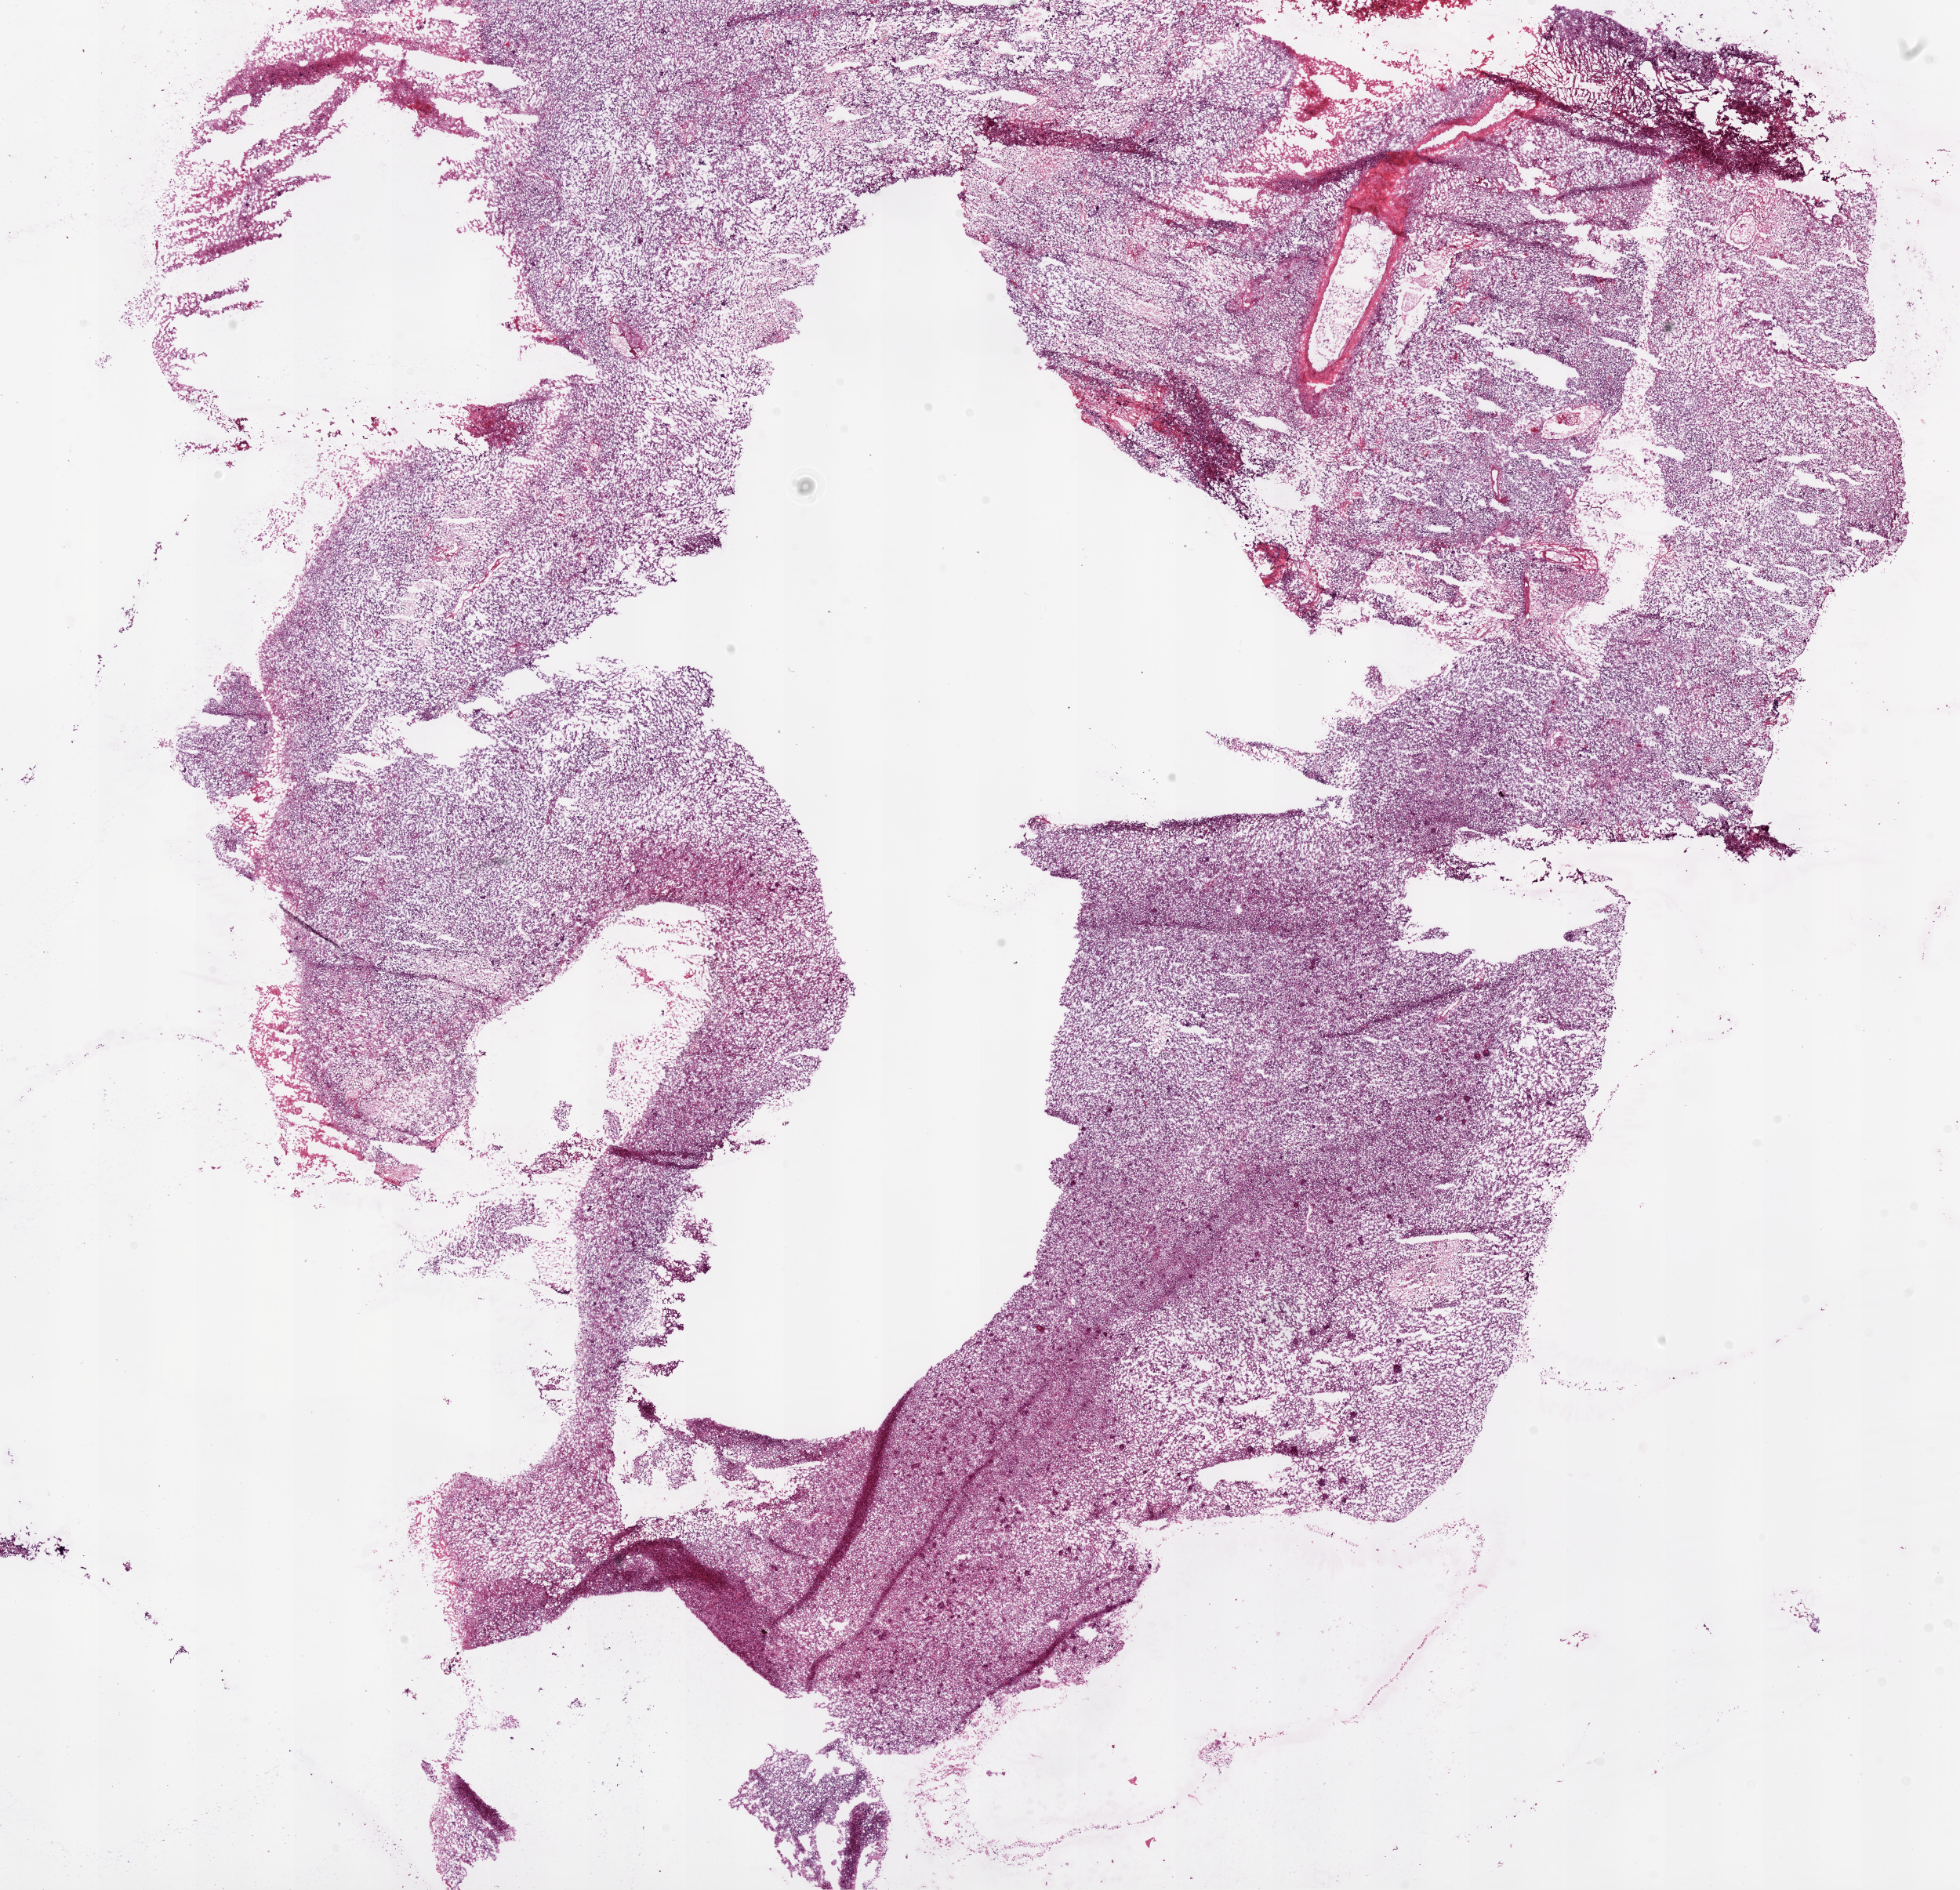
Whole-slide histology image, Hematoxylin and eosin (H&E) stained, whole scanned area (about 20.1 x 19.3 mm, from a 20x scan) shown as a low-resolution overview. Frozen section from the bottom of the tissue portion. Sample: primary tumour, brain. Male patient; age at initial diagnosis 53 years. Composition of this section per pathologist review: tumour cells 100%, tumour nuclei 80%, normal cells 0%, stromal cells 0%, necrosis 0%.
Diagnosis: Glioblastoma.